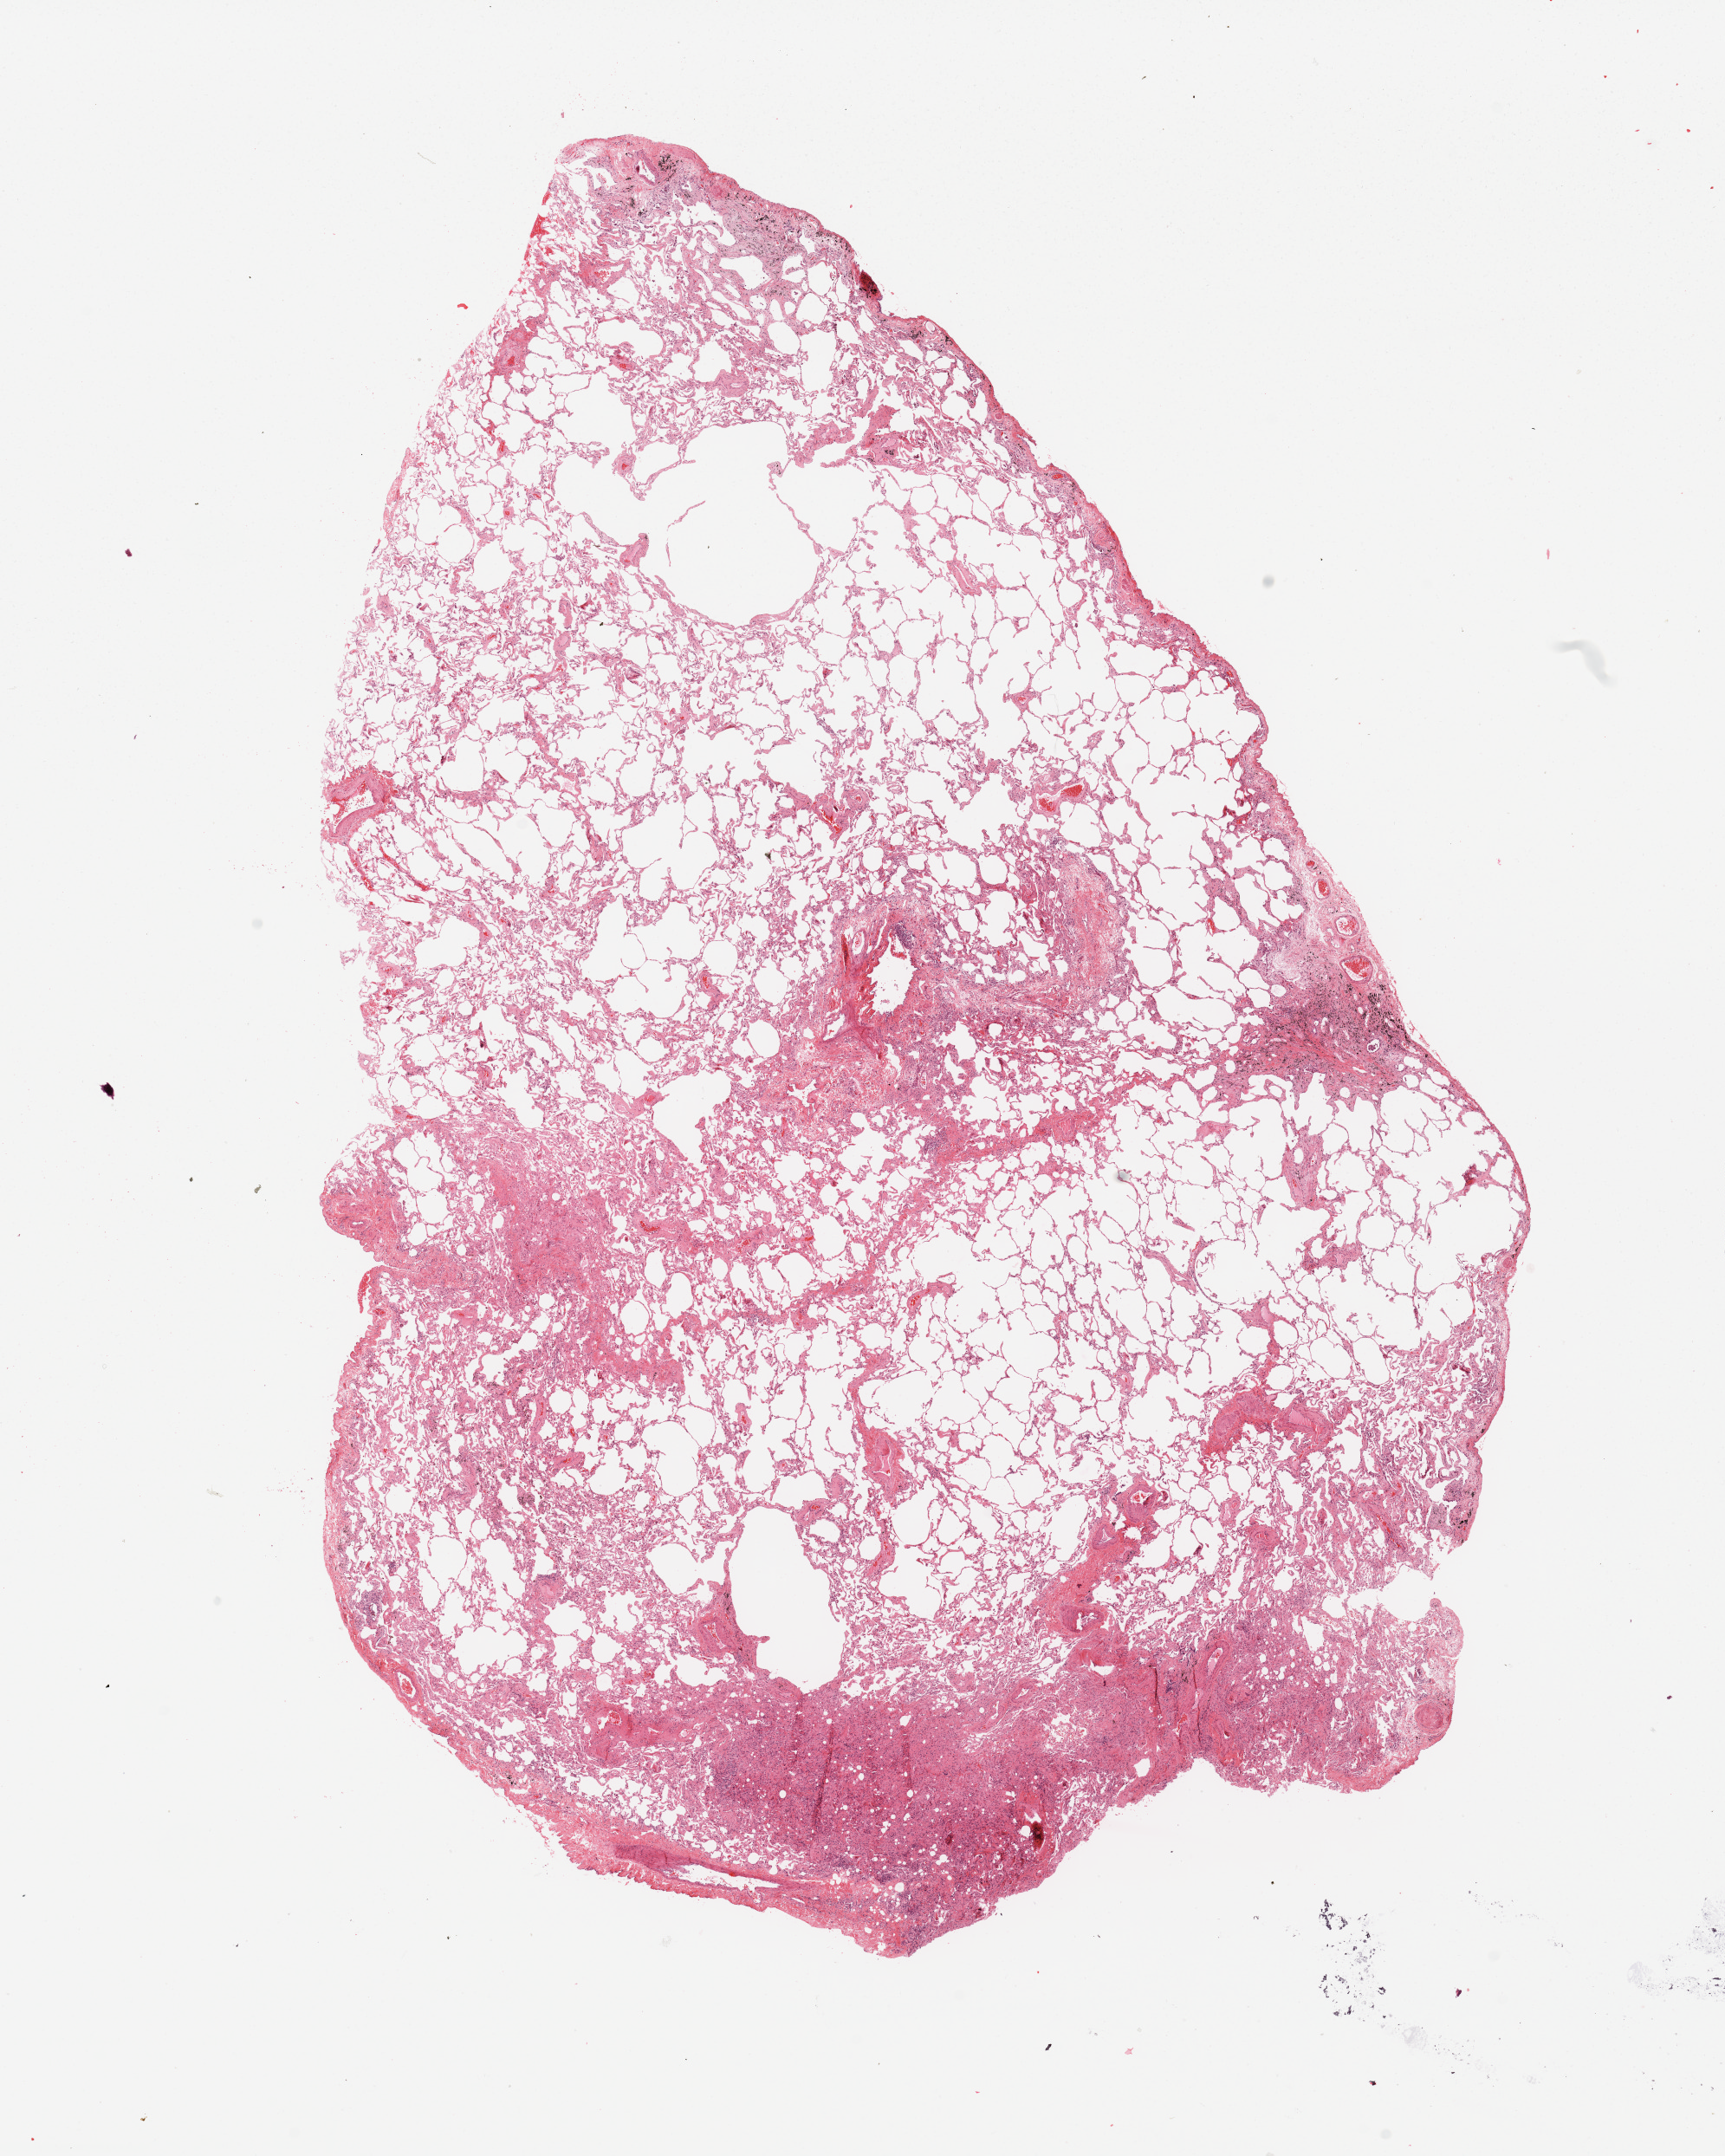
Digitized Hematoxylin and eosin (H&E) stained tissue section (whole slide), a low-resolution overview of the entire scanned area, about 15.8 x 19.7 mm (slide scanned at 20x), normal (non-tumour) tissue sample, sampled site: lung. Patient: male, age 69 years.
This section: normal (non-tumour) tissue from the same patient. Patient diagnosis: Squamous cell carcinoma, NOS.